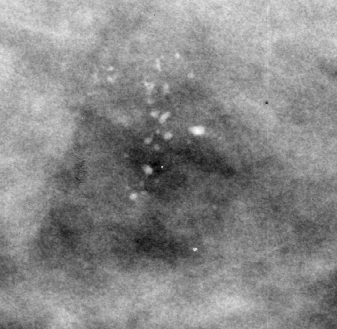
Cropped region of a digitized screen-film mammogram centred on a radiologist-marked abnormality; left breast; CC view.
Finding: calcifications, morphology pleomorphic, distribution clustered; BI-RADS assessment category 4; pathology result (as recorded, not read from the image): malignant.